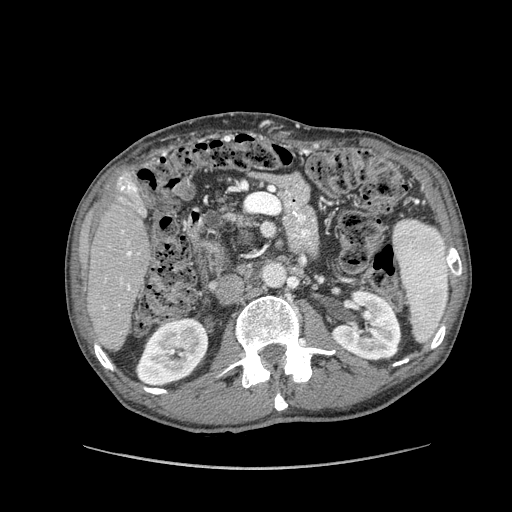
Contrast-enhanced abdominal CT (liver protocol), one axial slice; slice 37 of 162 in the series (ordered by position); soft-tissue window (W 400 / L 40 HU); 512 × 512 image matrix, field of view 400 × 400 mm. Case-level facts recorded for this patient, not image findings: diagnosis: hepatocellular carcinoma (patient treated with transarterial chemoembolisation; whether this scan precedes or follows treatment is not stated here); TNM stage (as recorded): Stage-IIIA; Child-Pugh class: A; tumour size: 9.9 cm.
Annotated regions visible in this slice (semi-automatically segmented with operator editing):
- liver parenchyma outside the tumour (the mass and vessels are separate outlines, so this box may not span the whole liver): bounding box <88,170,150,350> (left, top, right, bottom; pixels)
- liver vessels: <103,177,141,309>